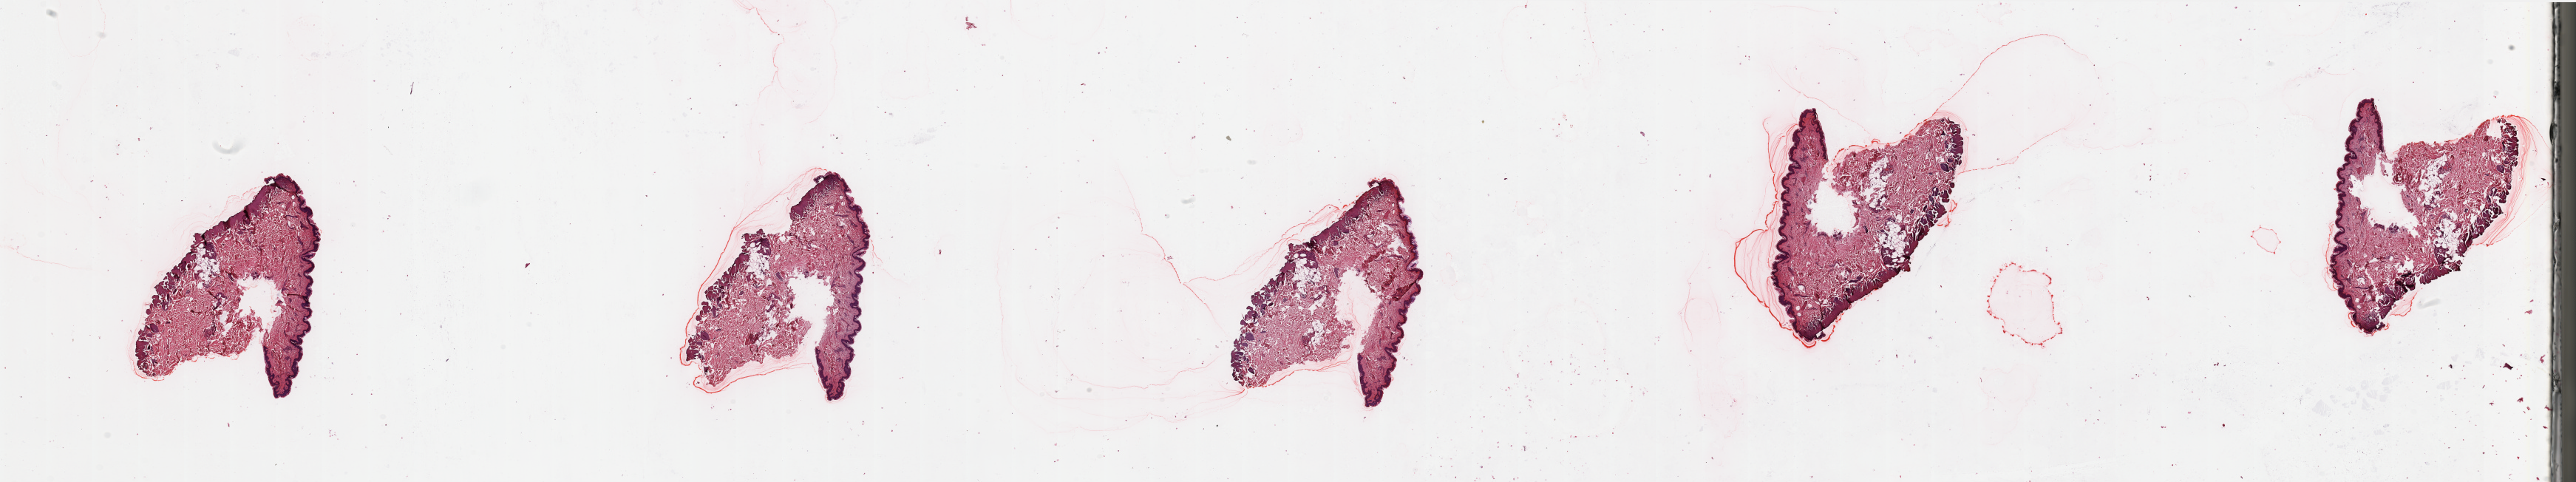
Whole-slide histology image, H&E — low-resolution overview of the scanned area, about 55.1 x 10.3 mm, normal (non-tumour) tissue sample, sampled site: trunk. Patient: male, age 42 years.
This section: normal (non-tumour) tissue from the same patient. Patient diagnosis: Malignant melanoma, NOS.